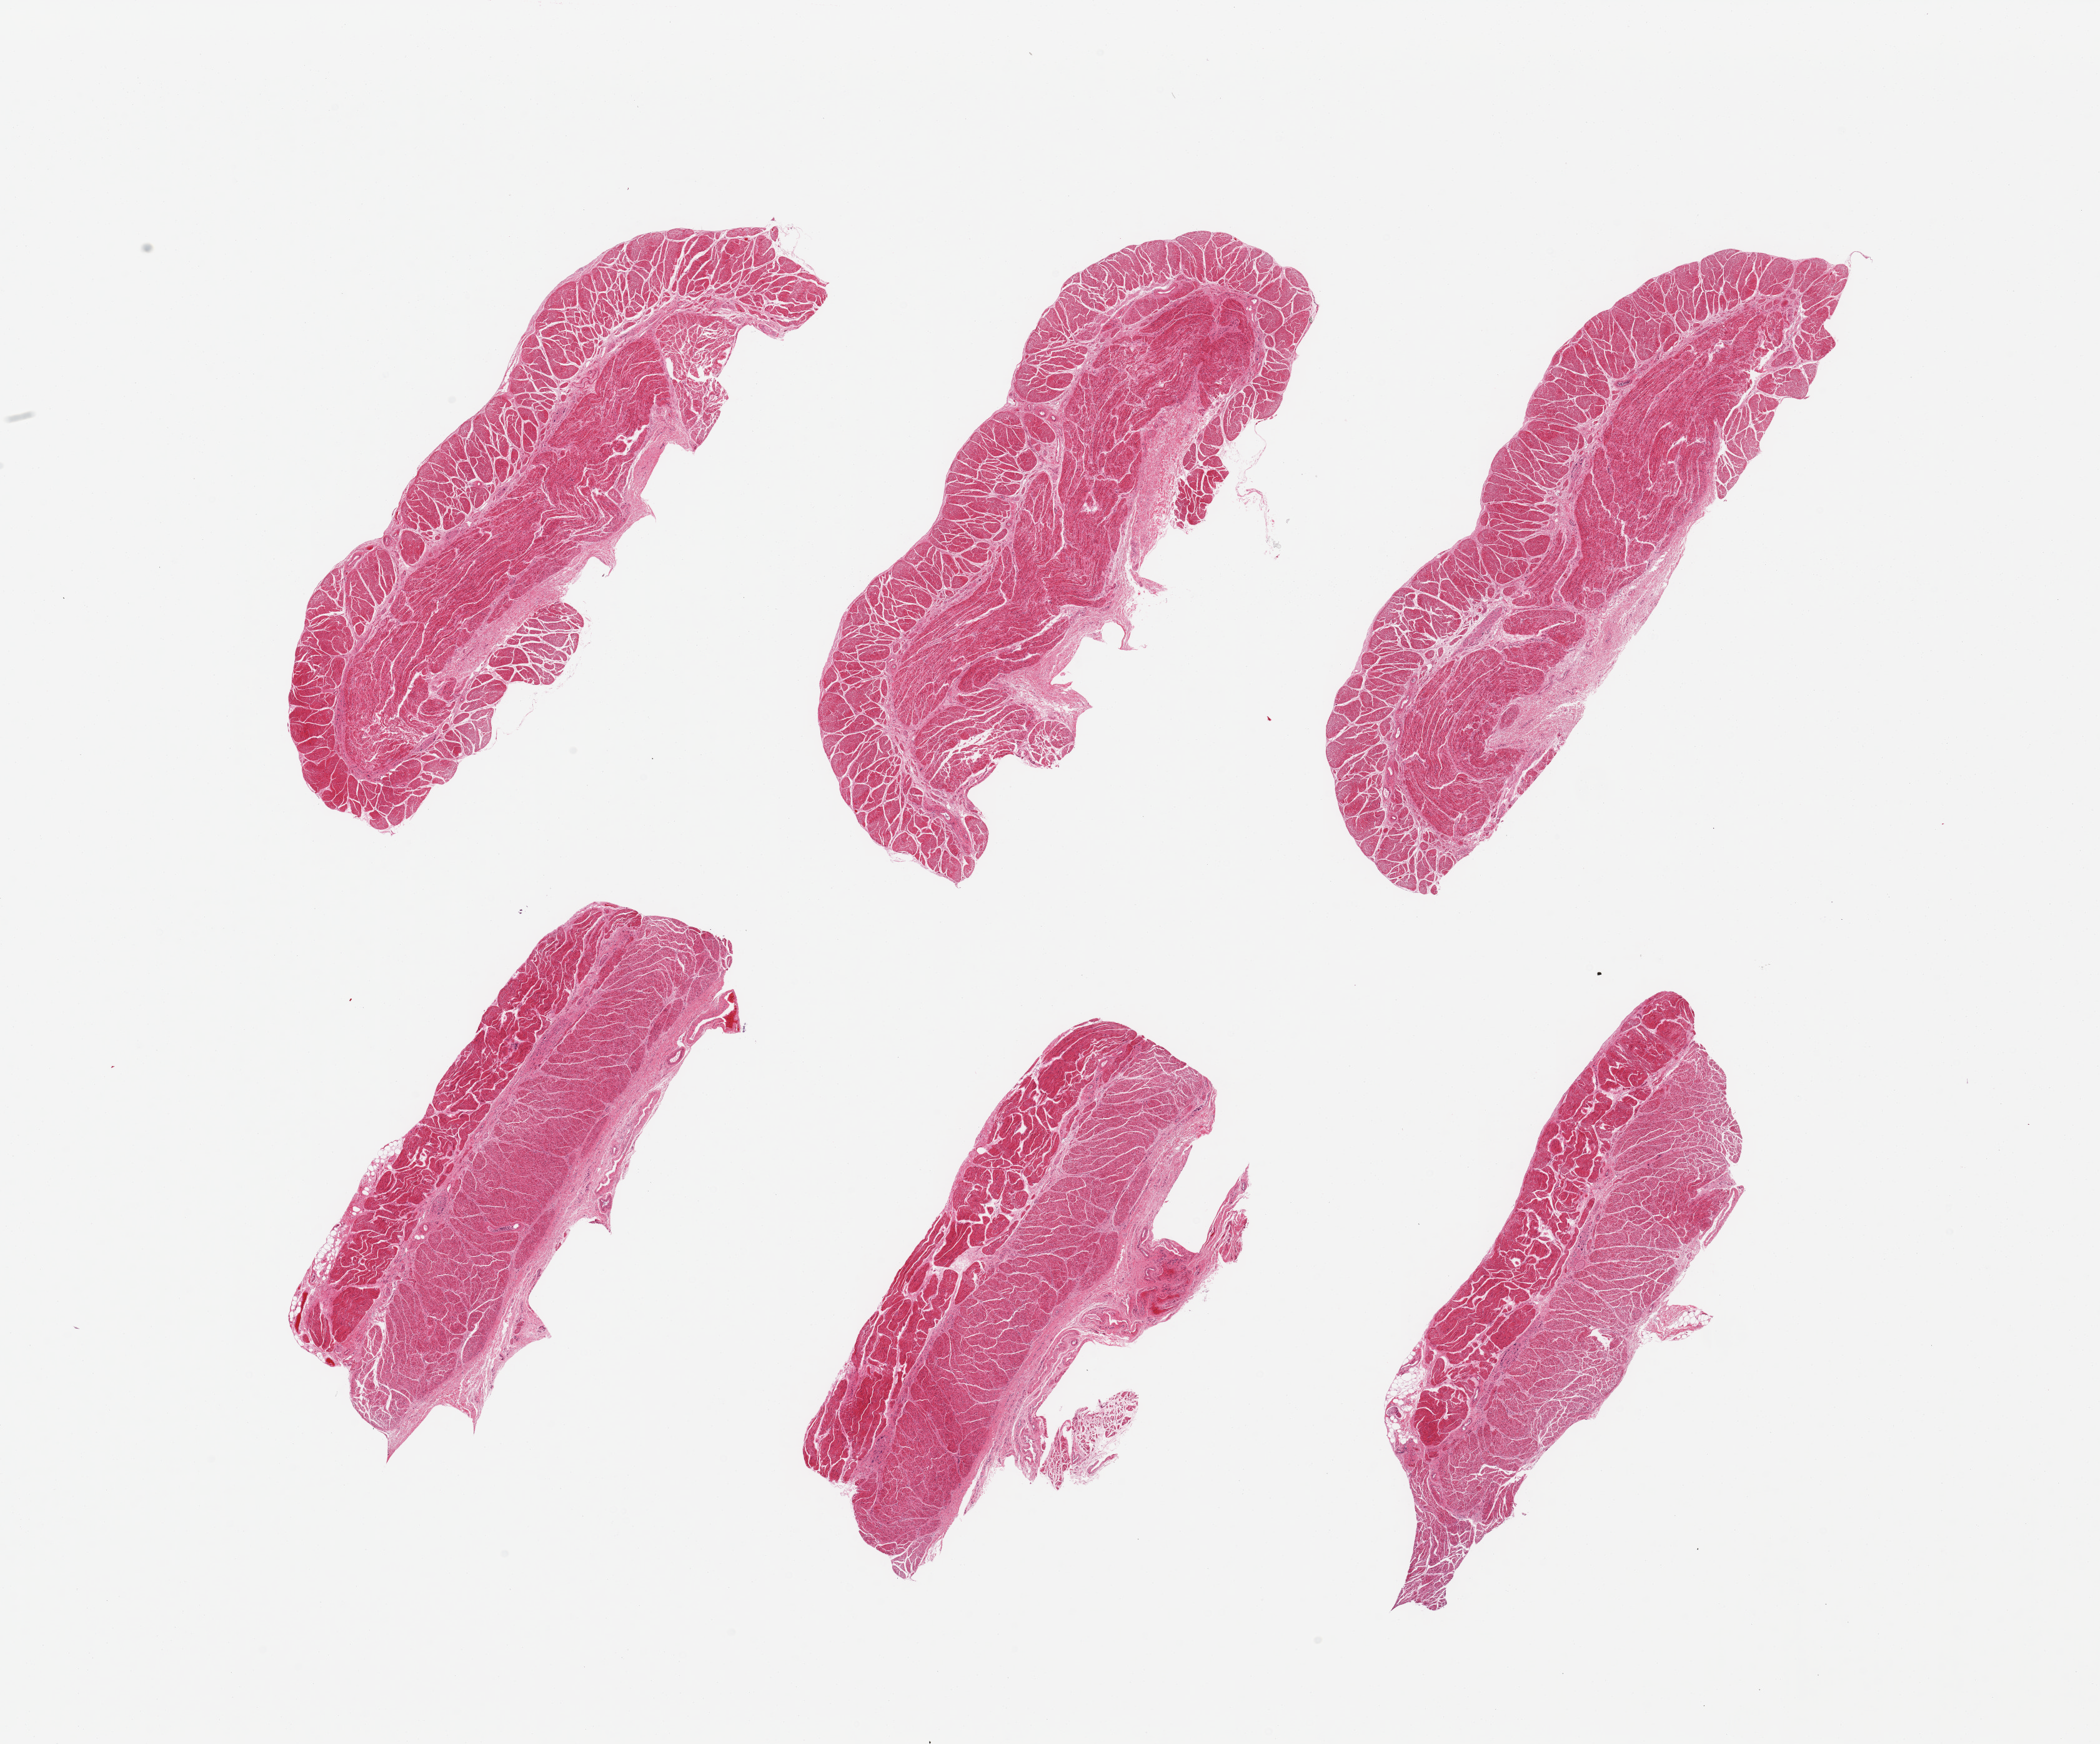
Whole-slide image, haematoxylin and eosin stain, brightfield — low-resolution overview of the scanned area, about 26.6 x 22.1 mm. PAXgene-fixed paraffin-embedded (PFPE) section. Target tissue: esophageal muscle. Tissue donor sample.
Reviewer comment on this tissue sample: 6 pieces; target muscularis.